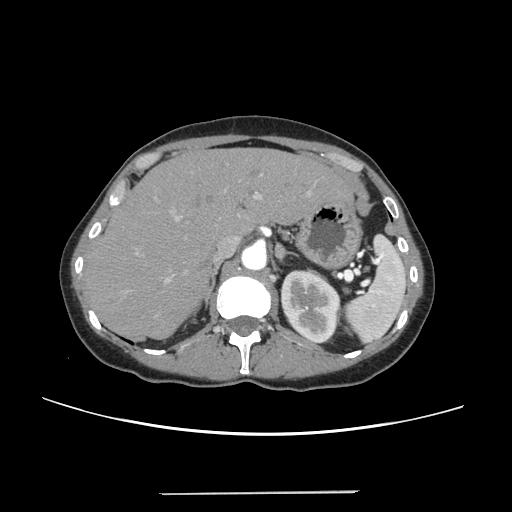
Contrast-enhanced abdominal CT, one axial slice; slice 171 of 240 in the series (ordered by position); intravenous contrast given; soft-tissue window (W 400 / L 40 HU); 1.25 mm slice thickness; 512 × 512 image matrix, field of view 371 × 371 mm. Female patient, age 60 years. From the clinical record (not read from this slice): diagnosis: colorectal cancer liver metastases, imaged before liver resection.
Annotated regions visible in this slice (expert manual segmentation):
- liver: bounding box [x1, y1, x2, y2] px = [86, 149, 349, 338]
- planned liver remnant (the part of the liver to remain after resection): [86, 149, 348, 338]
- portal vein (with intrahepatic branches): [136, 174, 310, 284]